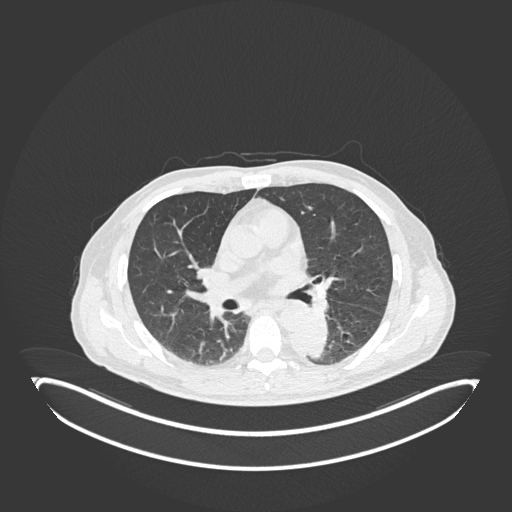
Chest CT, one axial slice; position 111 of 251 along the scan axis; reconstruction kernel B30f; lung window (W 1500 / L -600 HU); 512 × 512 image matrix. Patient: male, 72 years. Case-level facts recorded for this patient, not image findings: clinical TNM (as recorded): T2b N0 M1.
Outlined on this slice (rectangle marked by the reading radiologist):
- lung tumour (recorded histology: adenocarcinoma): bounding box <290,313,332,361> (left, top, right, bottom; pixels)